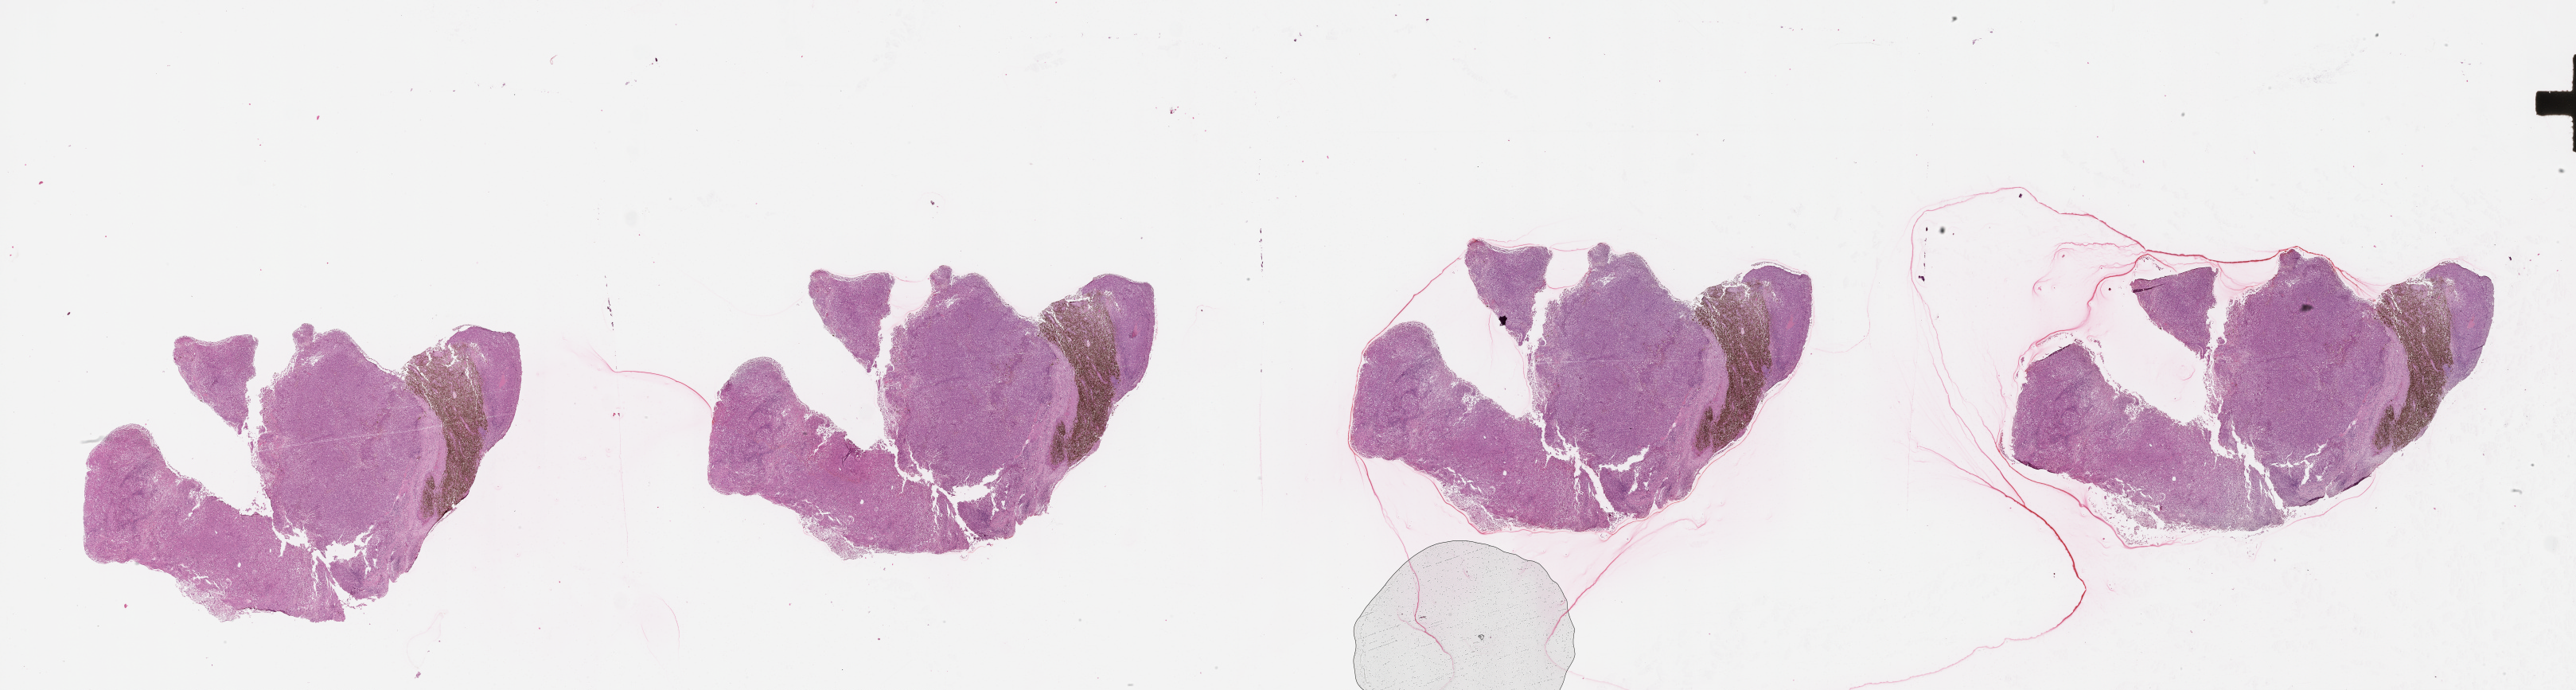
Whole-slide histology image, H&E-stained, whole scanned area (about 52.1 x 14.0 mm, from a 20x scan) shown as a low-resolution overview. Patient: male, age 87 years.
Patient diagnosis: Malignant melanoma, NOS.